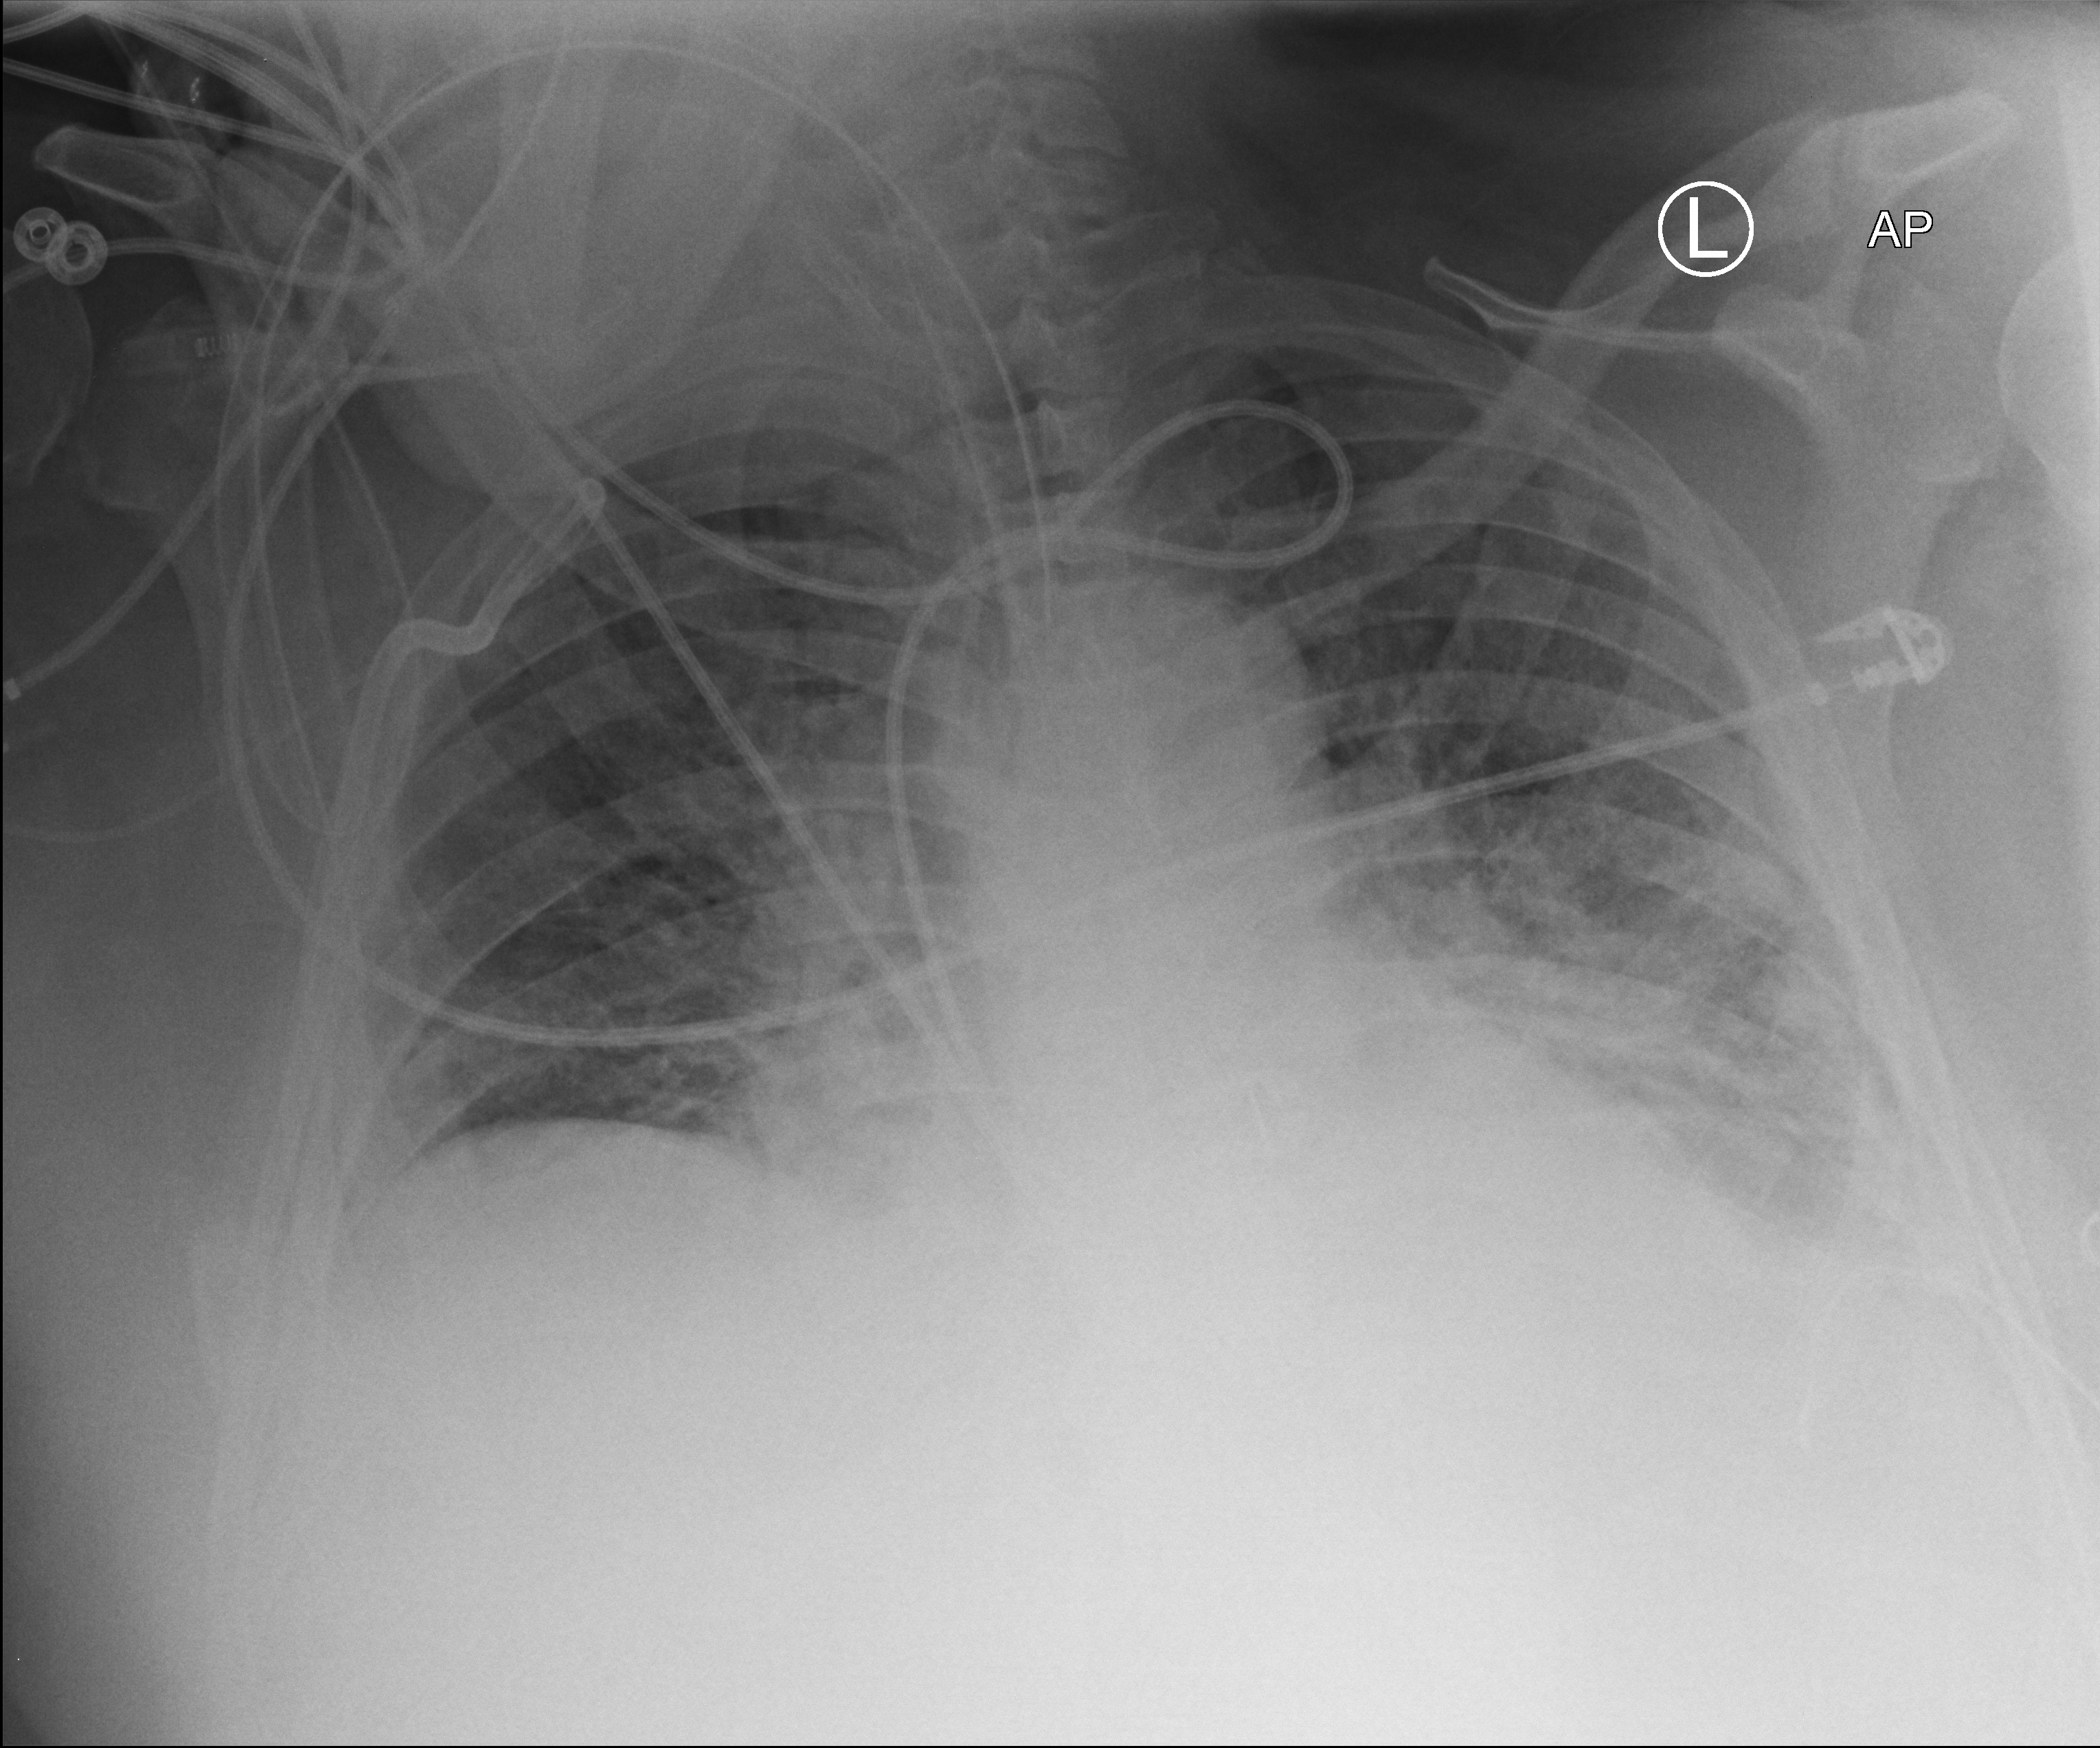
Bedside chest radiograph (computed radiography), anteroposterior (AP) projection. Male patient hospitalised with COVID-19, age 60–74 years.
Admission-level facts for this patient (not findings on this image; timing relative to this image not recorded): admitted to intensive care during this hospital stay: yes.